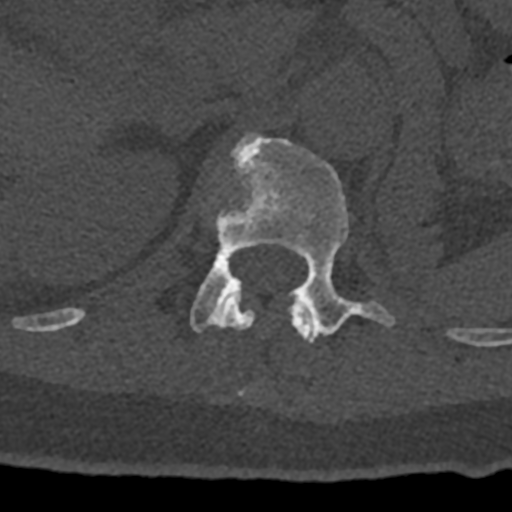
CT including the spine, one axial slice. Slice 455 of 797 in the series (ordered by position). Reconstruction kernel Br40s/3. 120 kVp. Bone window (W 1800 / L 400 HU). 512 × 512 image matrix. Male patient, age 74 years. Case-level facts recorded for this patient, not image findings: primary cancer: renal; vertebrae with lytic lesions (as recorded): T10, L1, L2, L3, L4, L5.
Outlined on this slice (semi-automatic segmentation, software-assisted and operator-edited):
- L1 vertebra: box from (x=190, y=133) to (x=394, y=341) px
- T12 vertebra: (x=70, y=298)–(x=314, y=343)